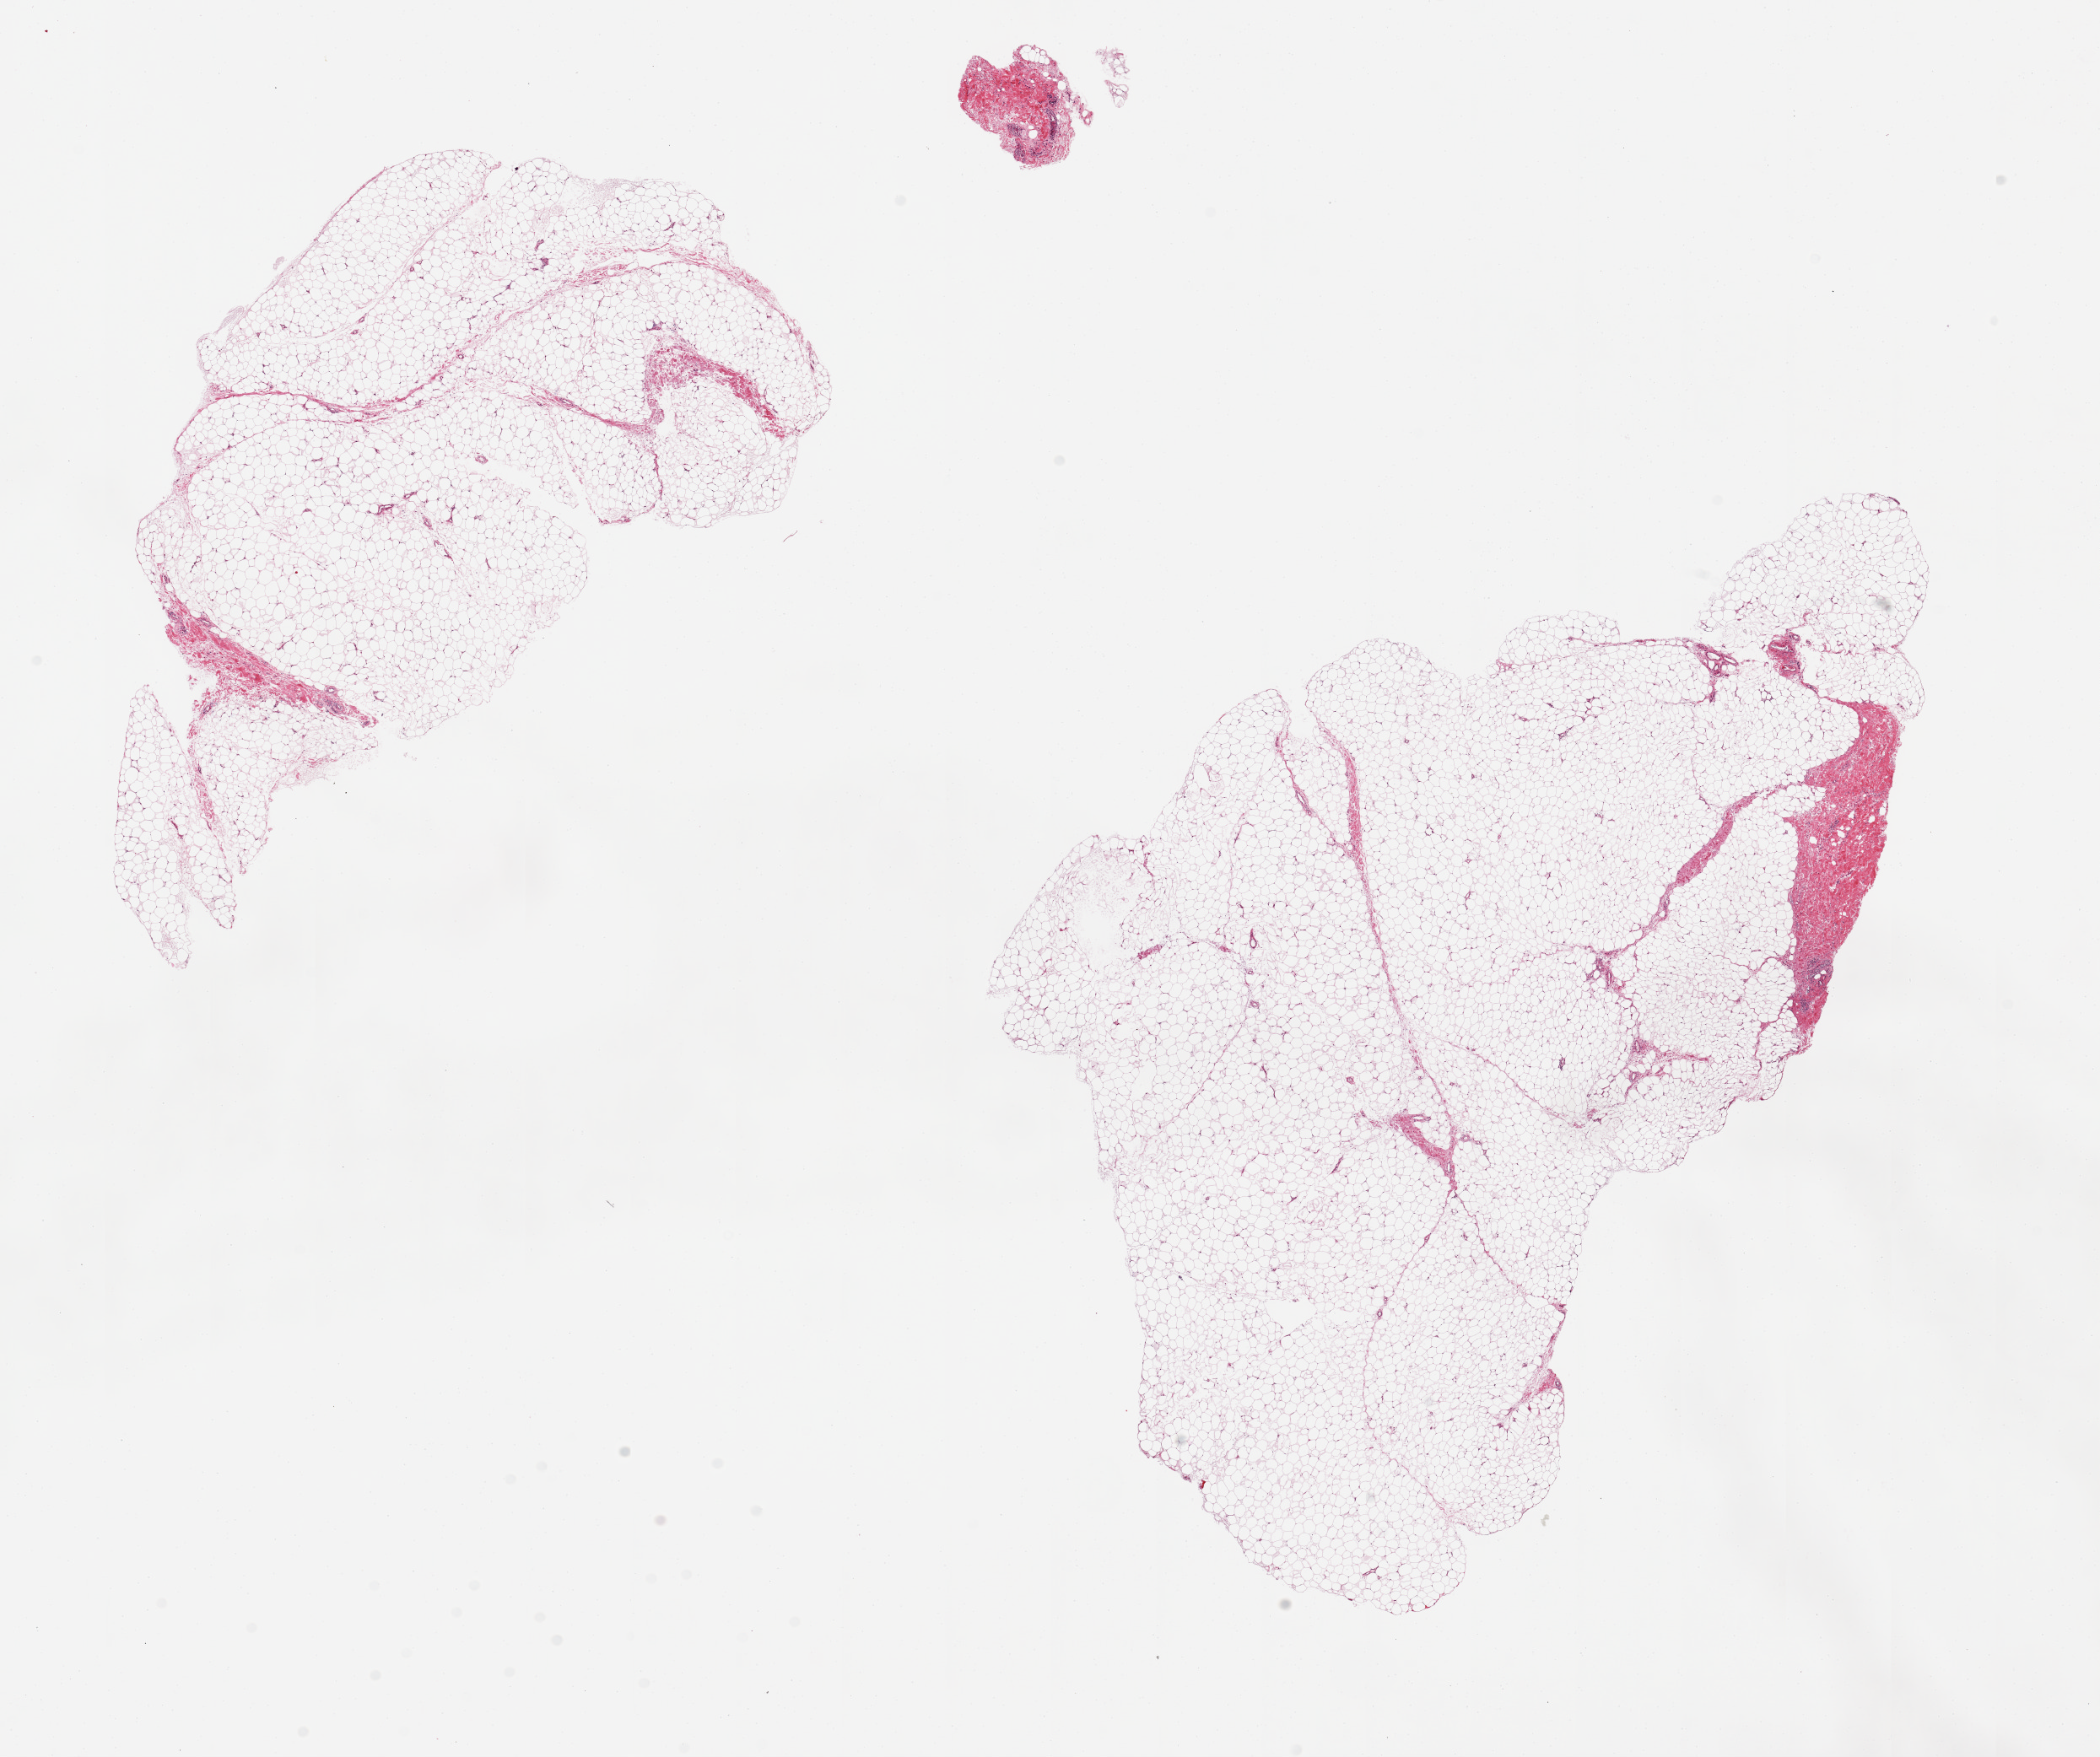
Digitized hematoxylin and eosin (H&E)-stained section, brightfield, a low-resolution overview of the entire scanned area, about 19.7 x 16.5 mm; PAXgene-fixed, paraffin-embedded tissue; sampled site (target tissue): omentum; donor tissue sample. Donor: female.
- pathologist's review note for this sample: 2 pieces, 9x5 & 12x7mm